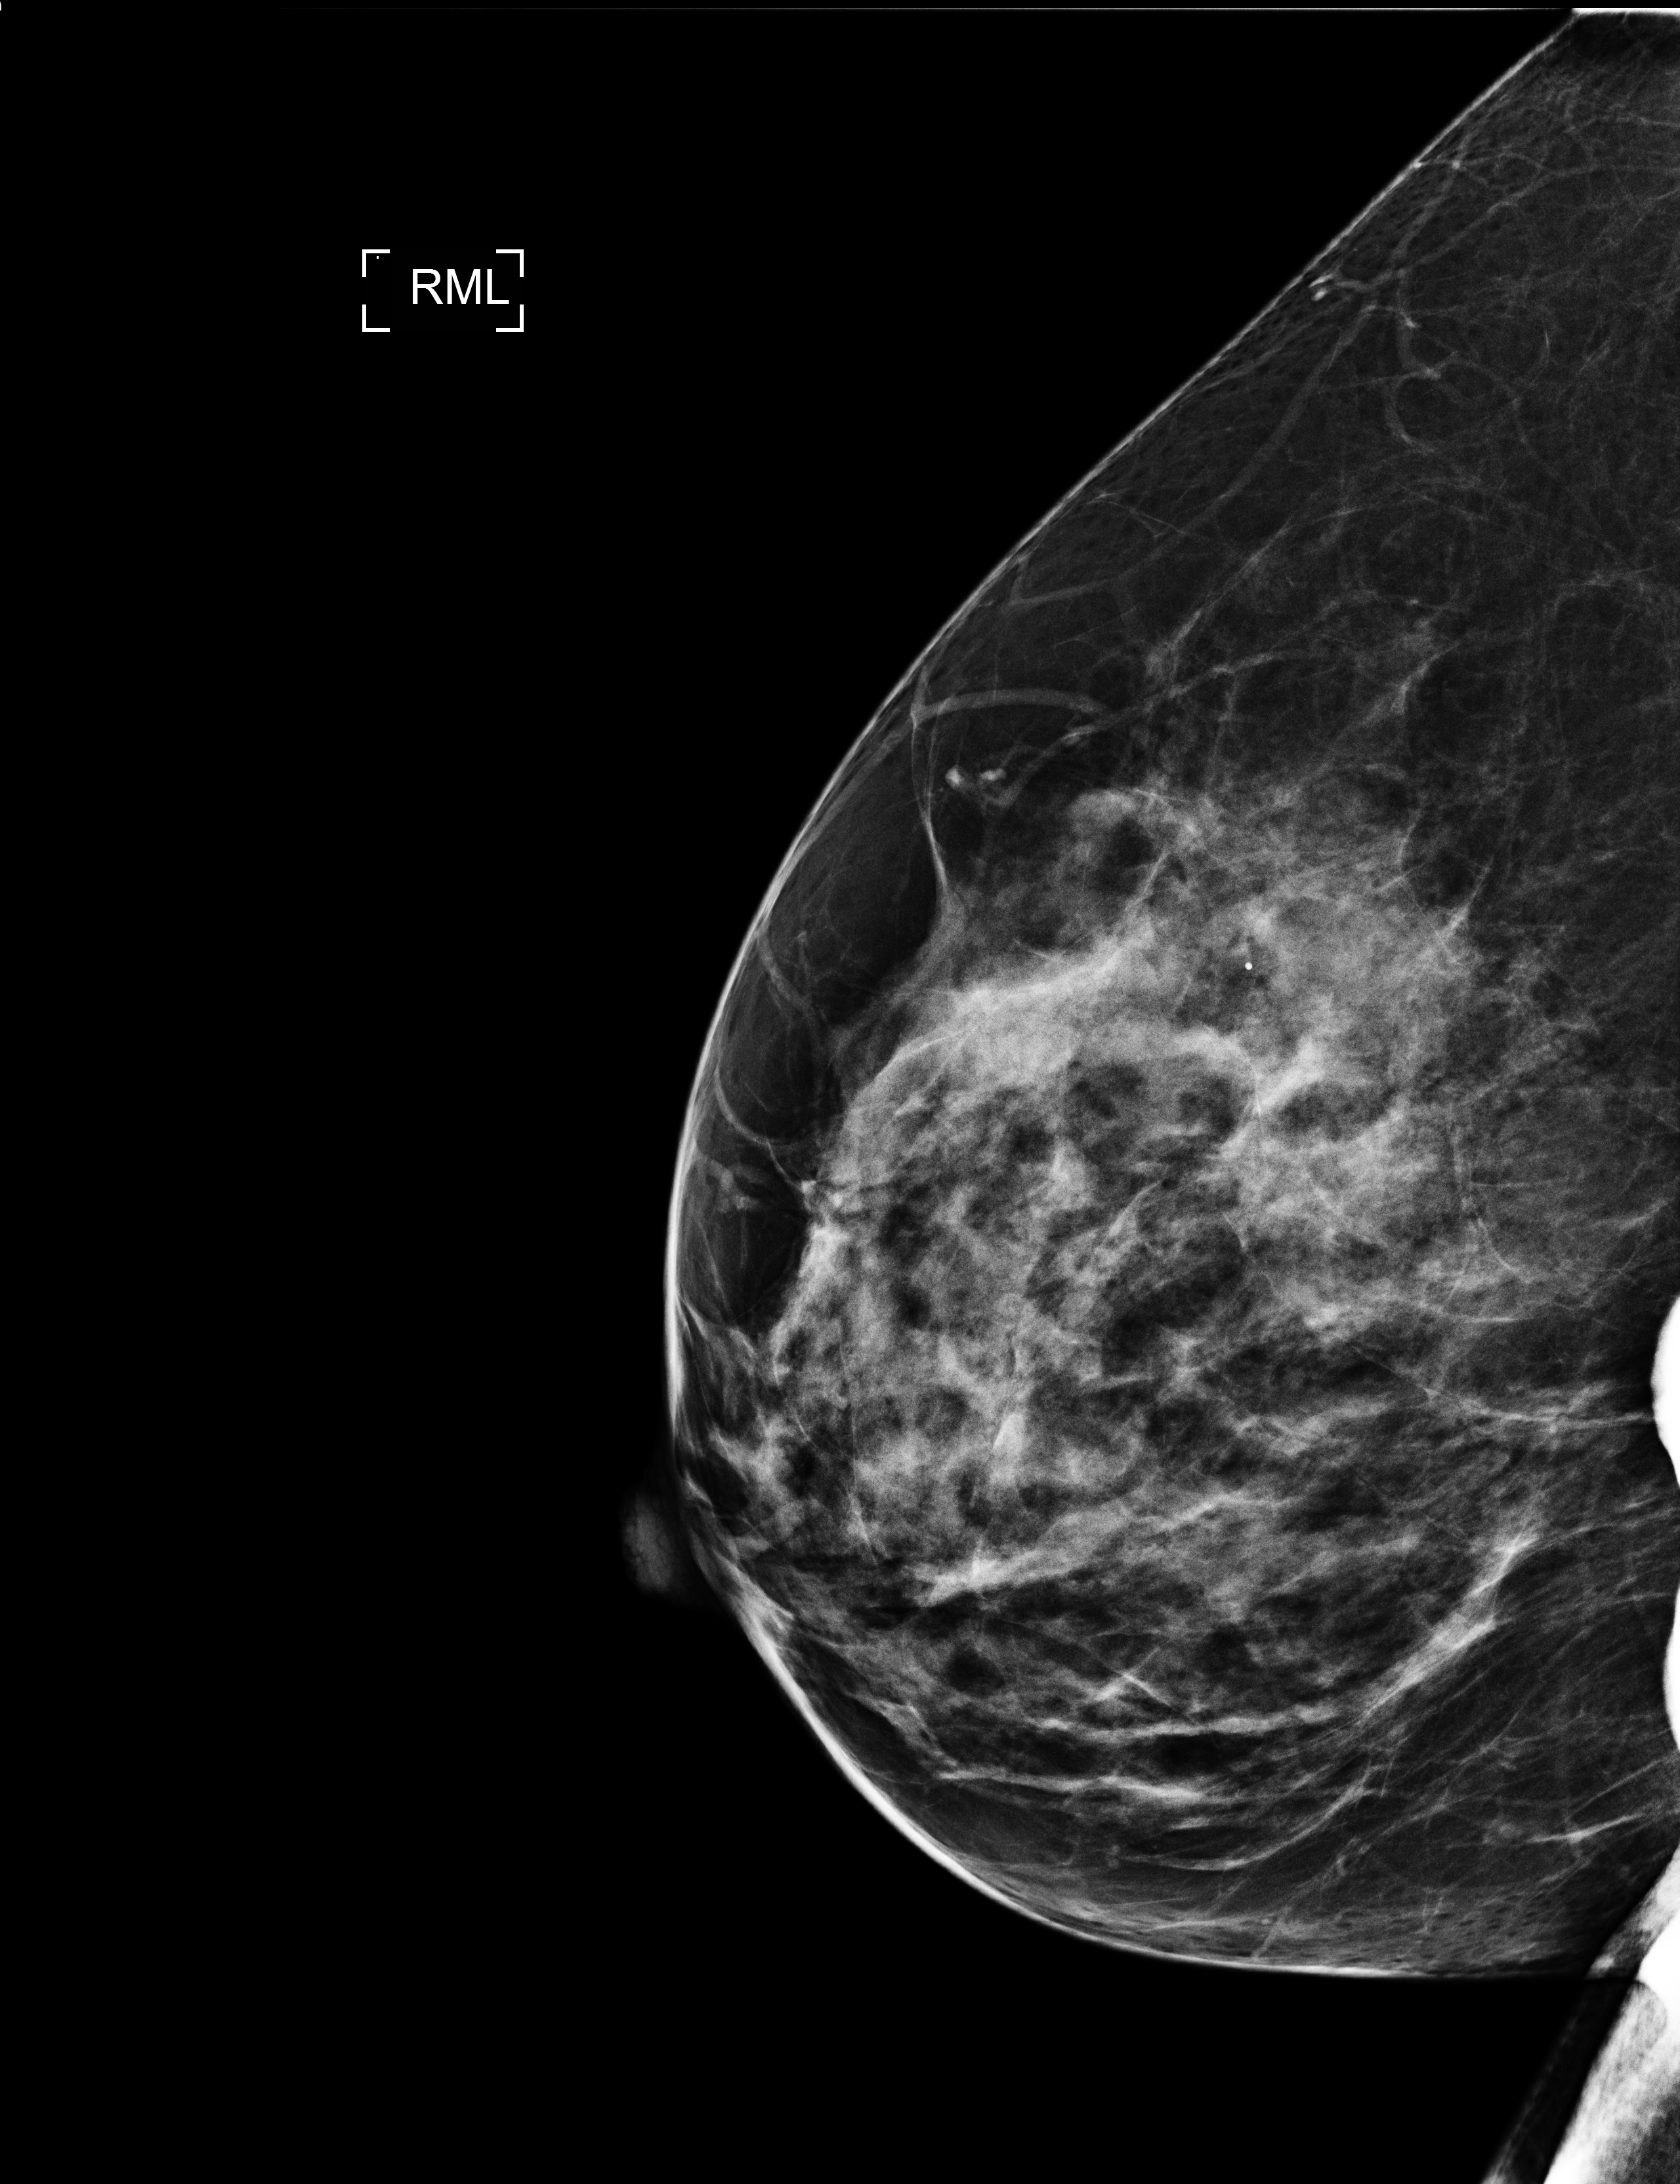
Diagnostic work-up study, compressed breast thickness 52 mm. Patient aged 41 years (female).
Image type: full-field digital mammogram. Breast: right. Projection: ML view.